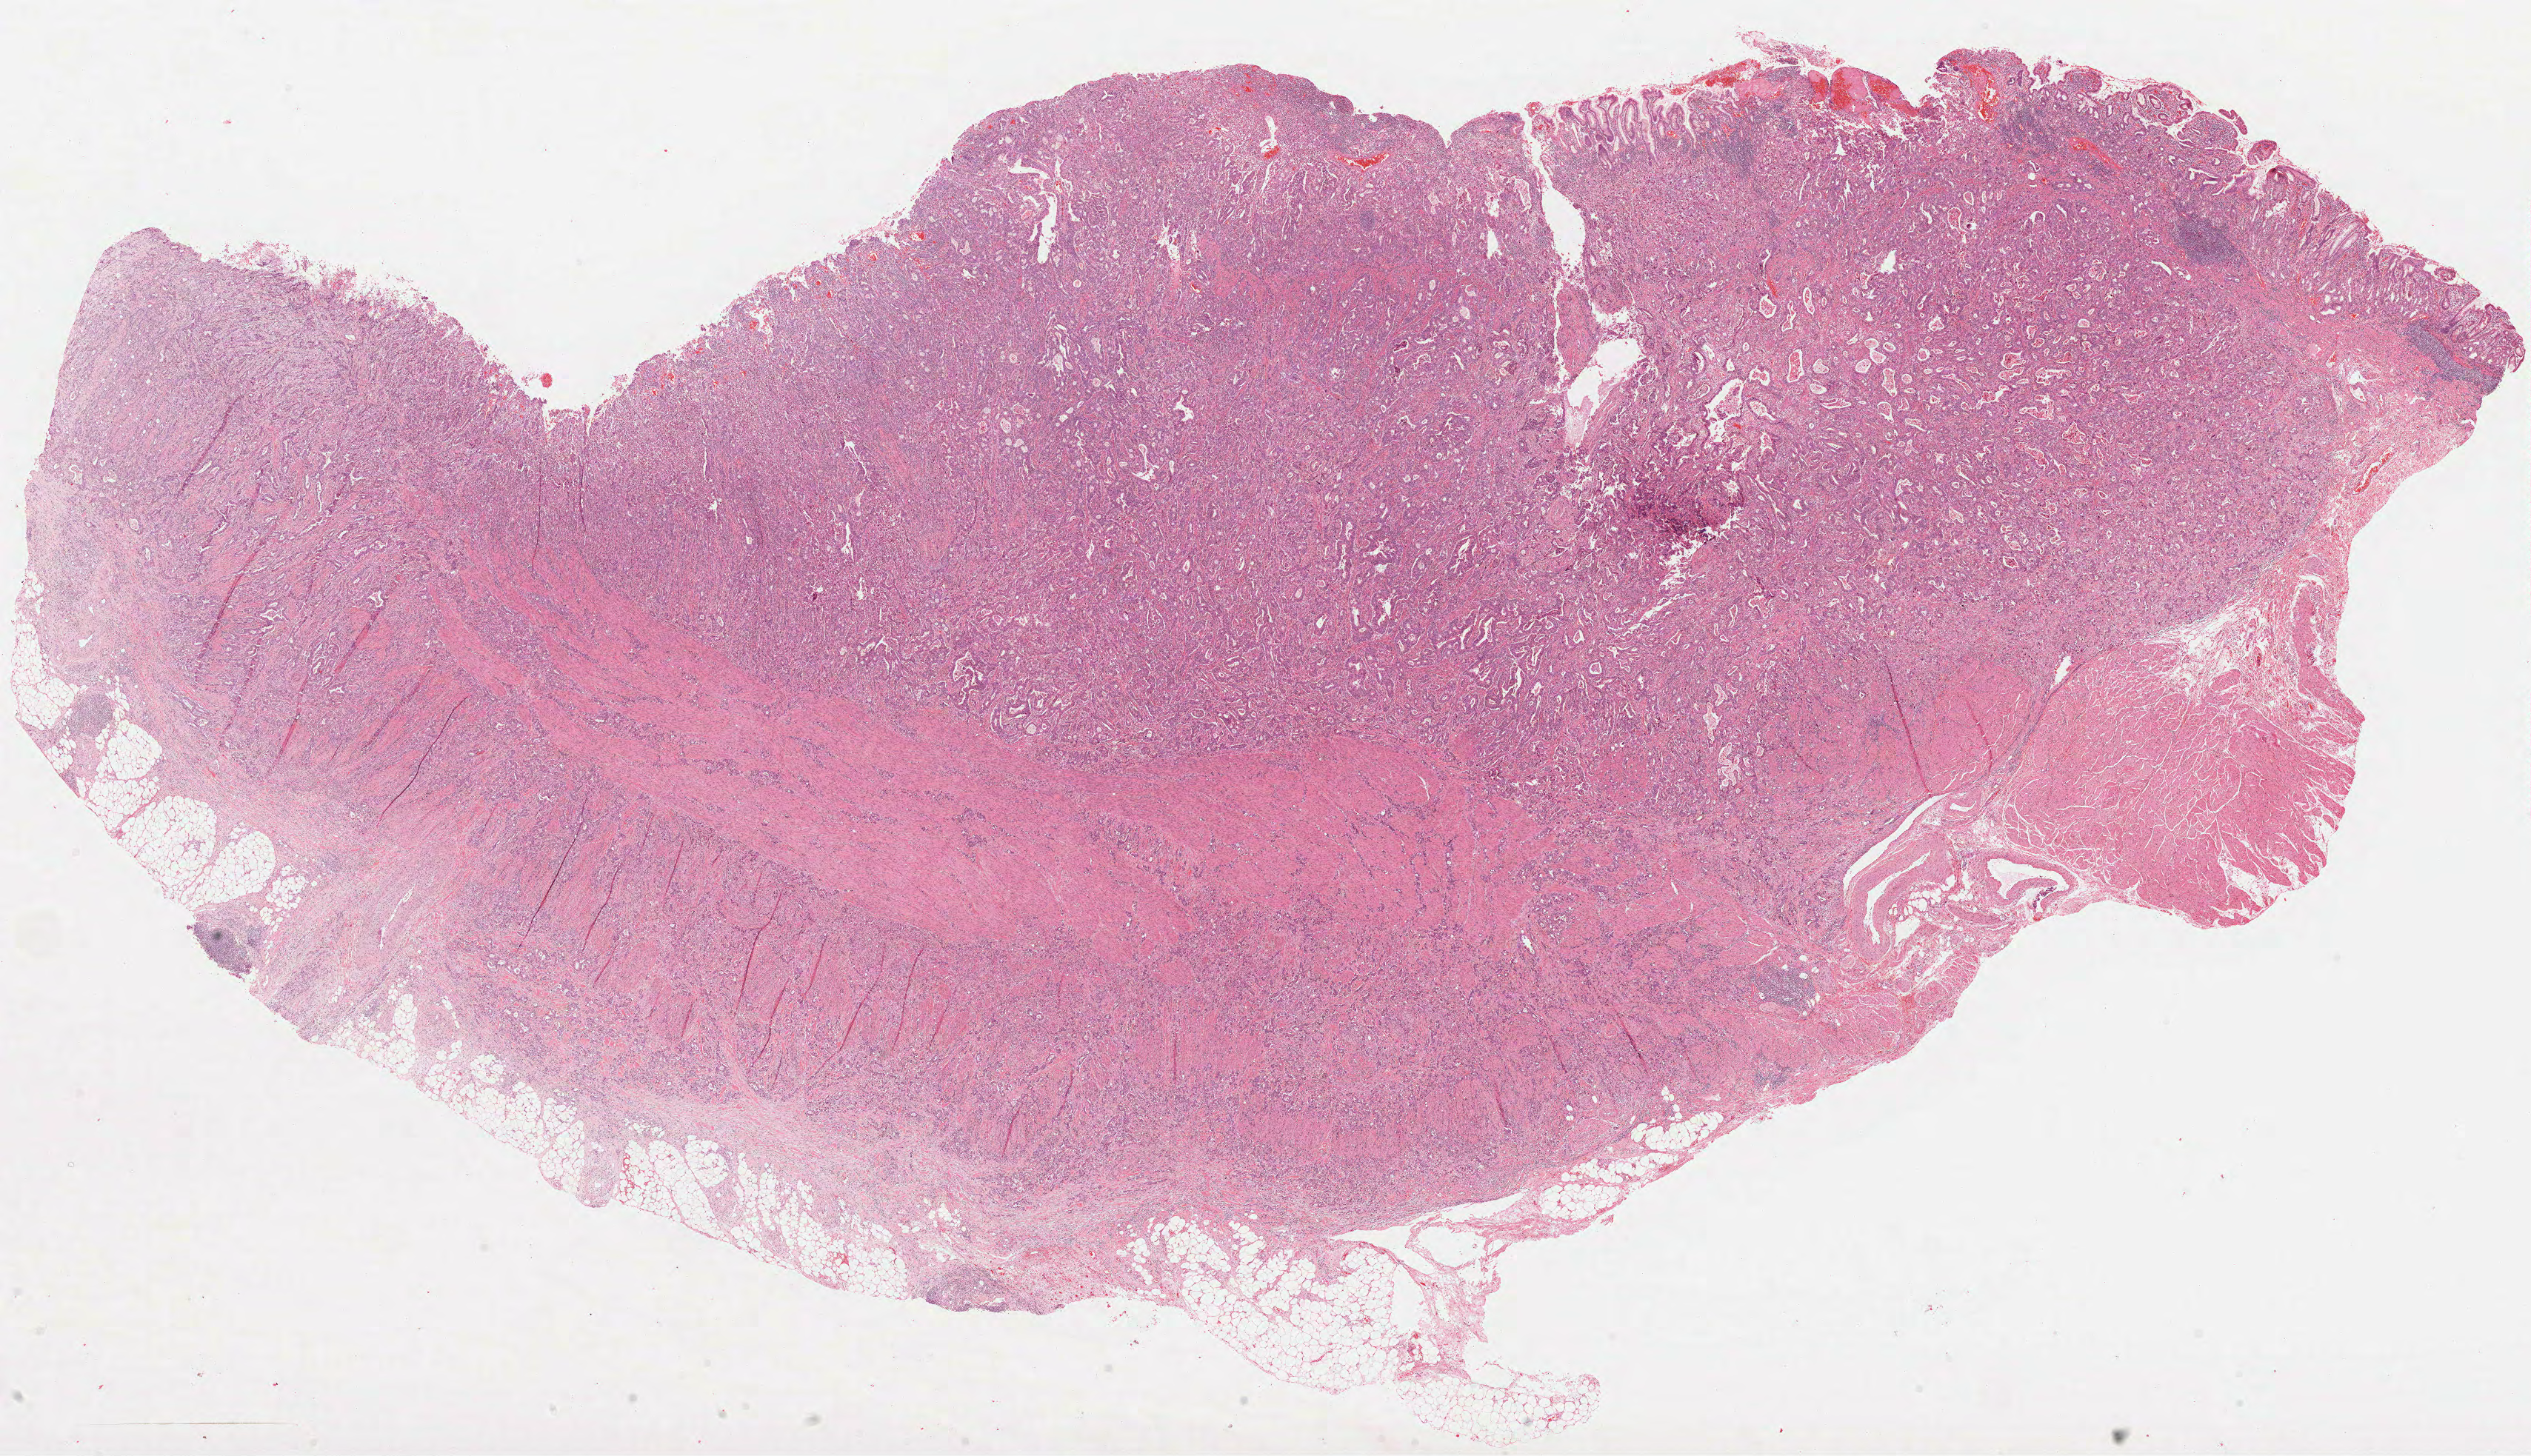
Hematoxylin and eosin (H&E) stained whole-slide image — low-resolution overview of the scanned area, about 27.6 x 15.9 mm (from a 40x scan). Formalin-fixed paraffin-embedded (FFPE) diagnostic section. Sample: primary tumour, stomach. Female patient; age at initial diagnosis 74 years. Histologic grade: G2 (moderately differentiated).
- histologic diagnosis: Adenocarcinoma, NOS
- AJCC pathologic stage: IIB (7th edition)